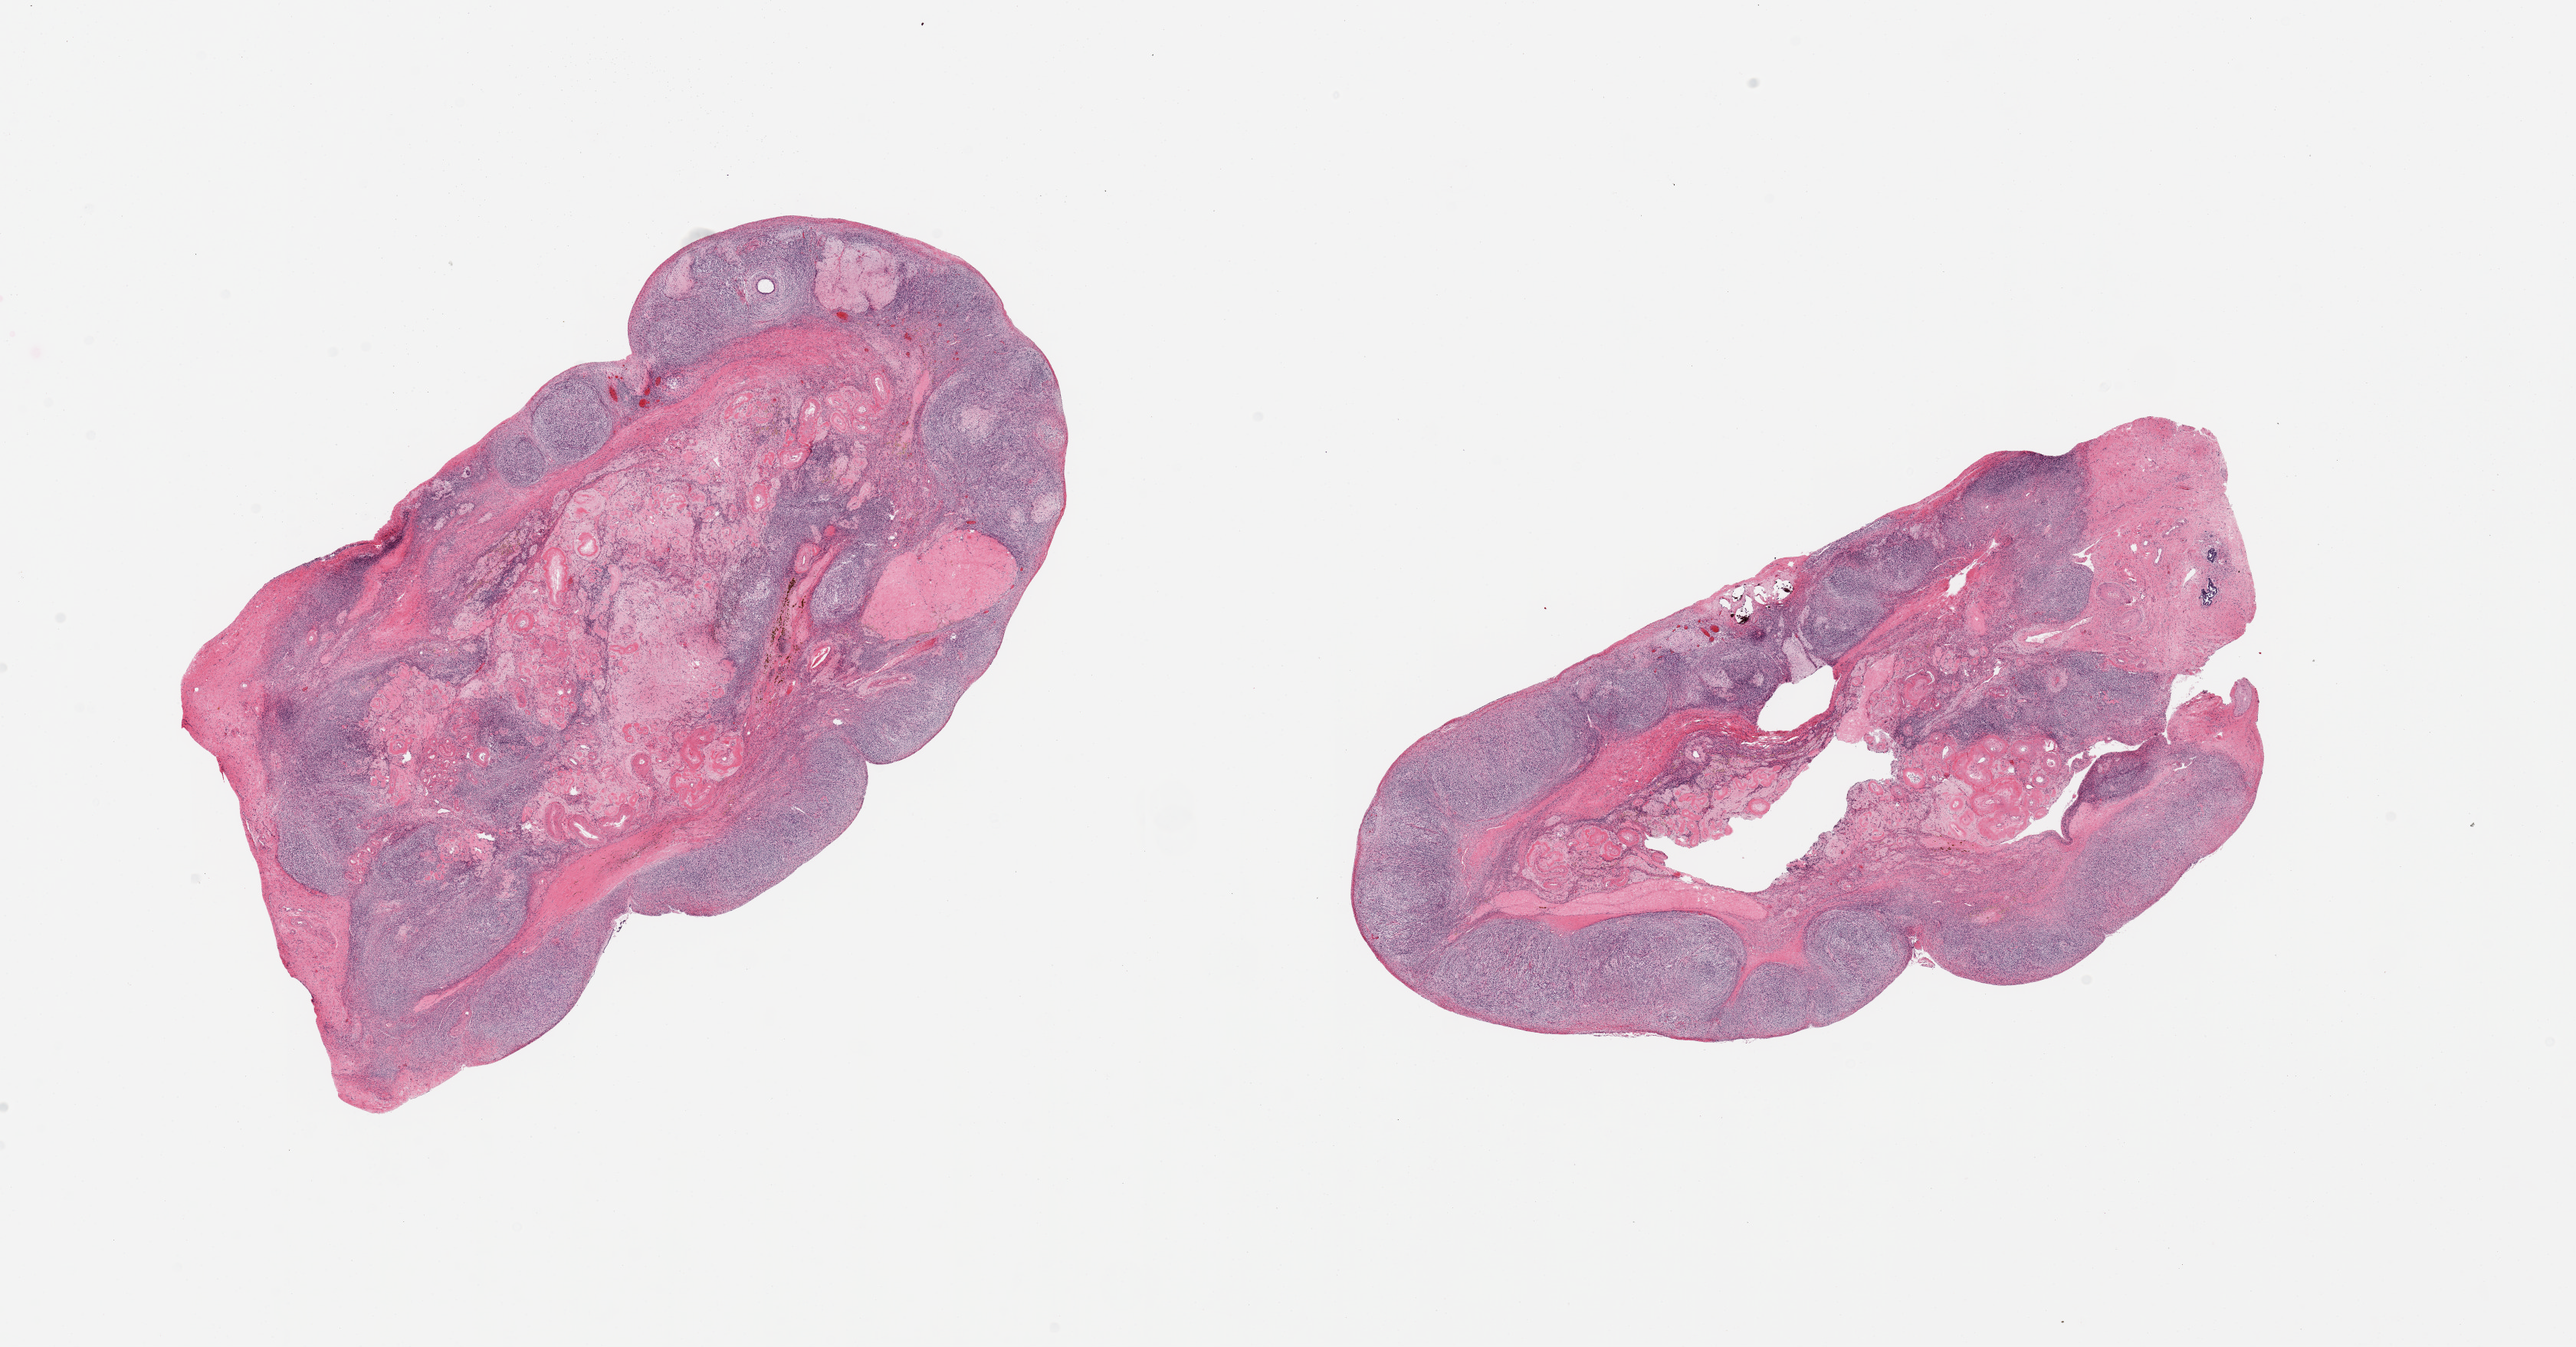
Whole-slide image, haematoxylin and eosin stain — a low-resolution overview of the entire scanned area, about 26.6 x 13.9 mm (slide scanned at 20x); PAXgene-fixed, paraffin-embedded tissue; sampled site (target tissue): ovary; donor tissue sample. Donor: female.
Review note (as recorded): 2 pieces, corpora albicantia/fibrosa, numerous thick-walled vessels with amyloid-like material.